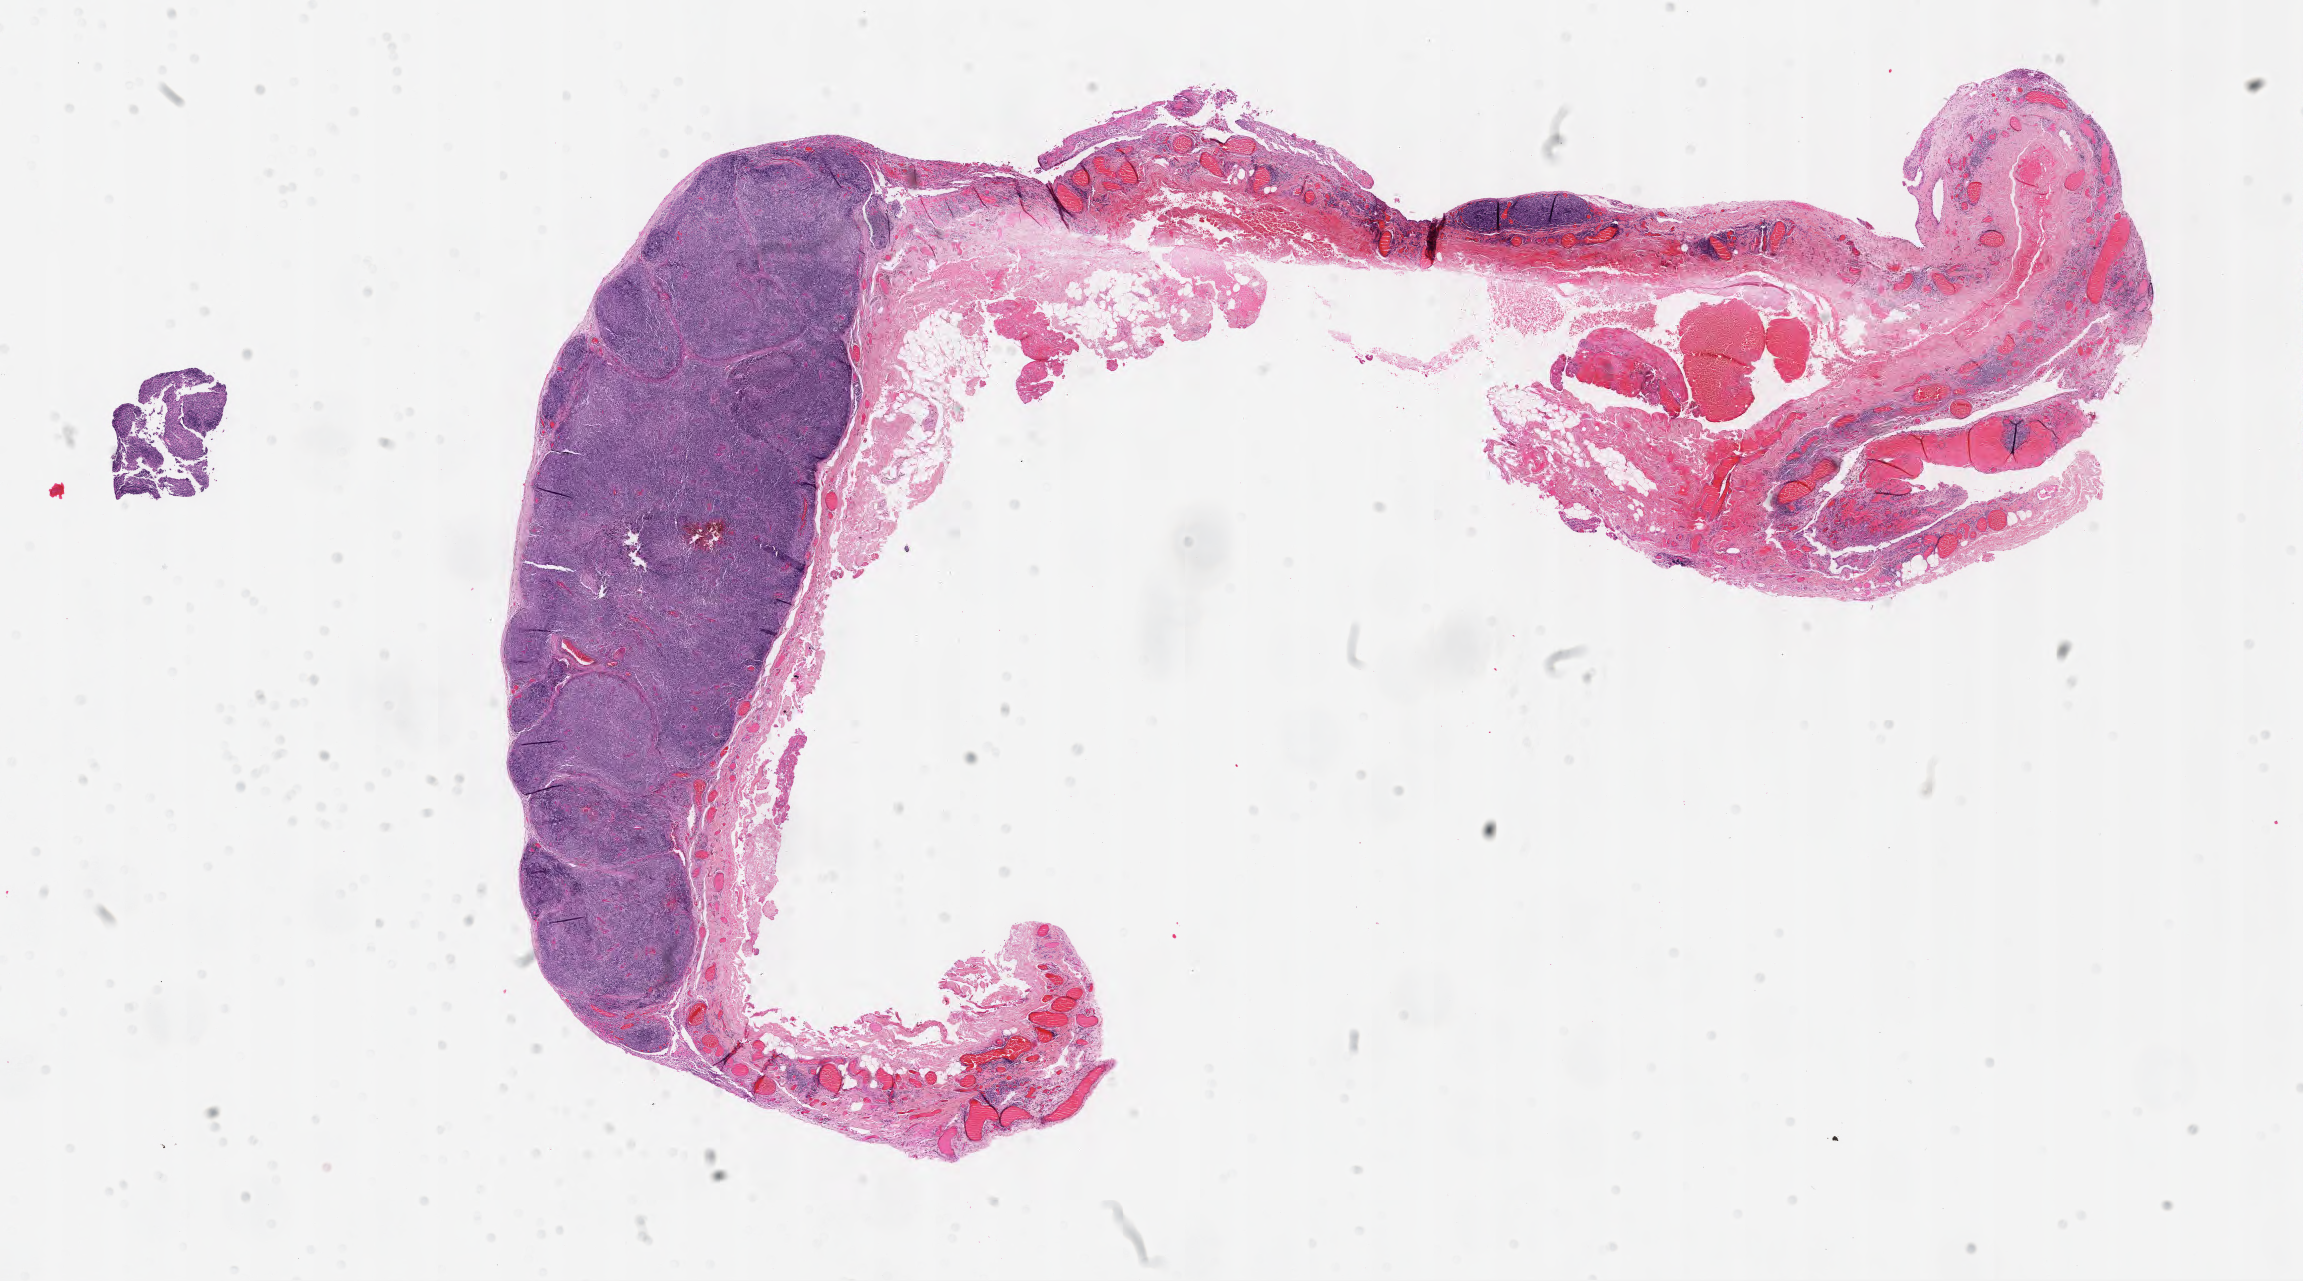
H&E whole-slide image, whole scanned area (about 18.6 x 10.4 mm, acquisition: 40x scan) shown as a low-resolution overview, formalin-fixed paraffin-embedded (FFPE) diagnostic section, thymus, primary tumour sample. Patient: male, age at initial diagnosis 45 years.
Histologic diagnosis: Thymoma, type B1, malignant.